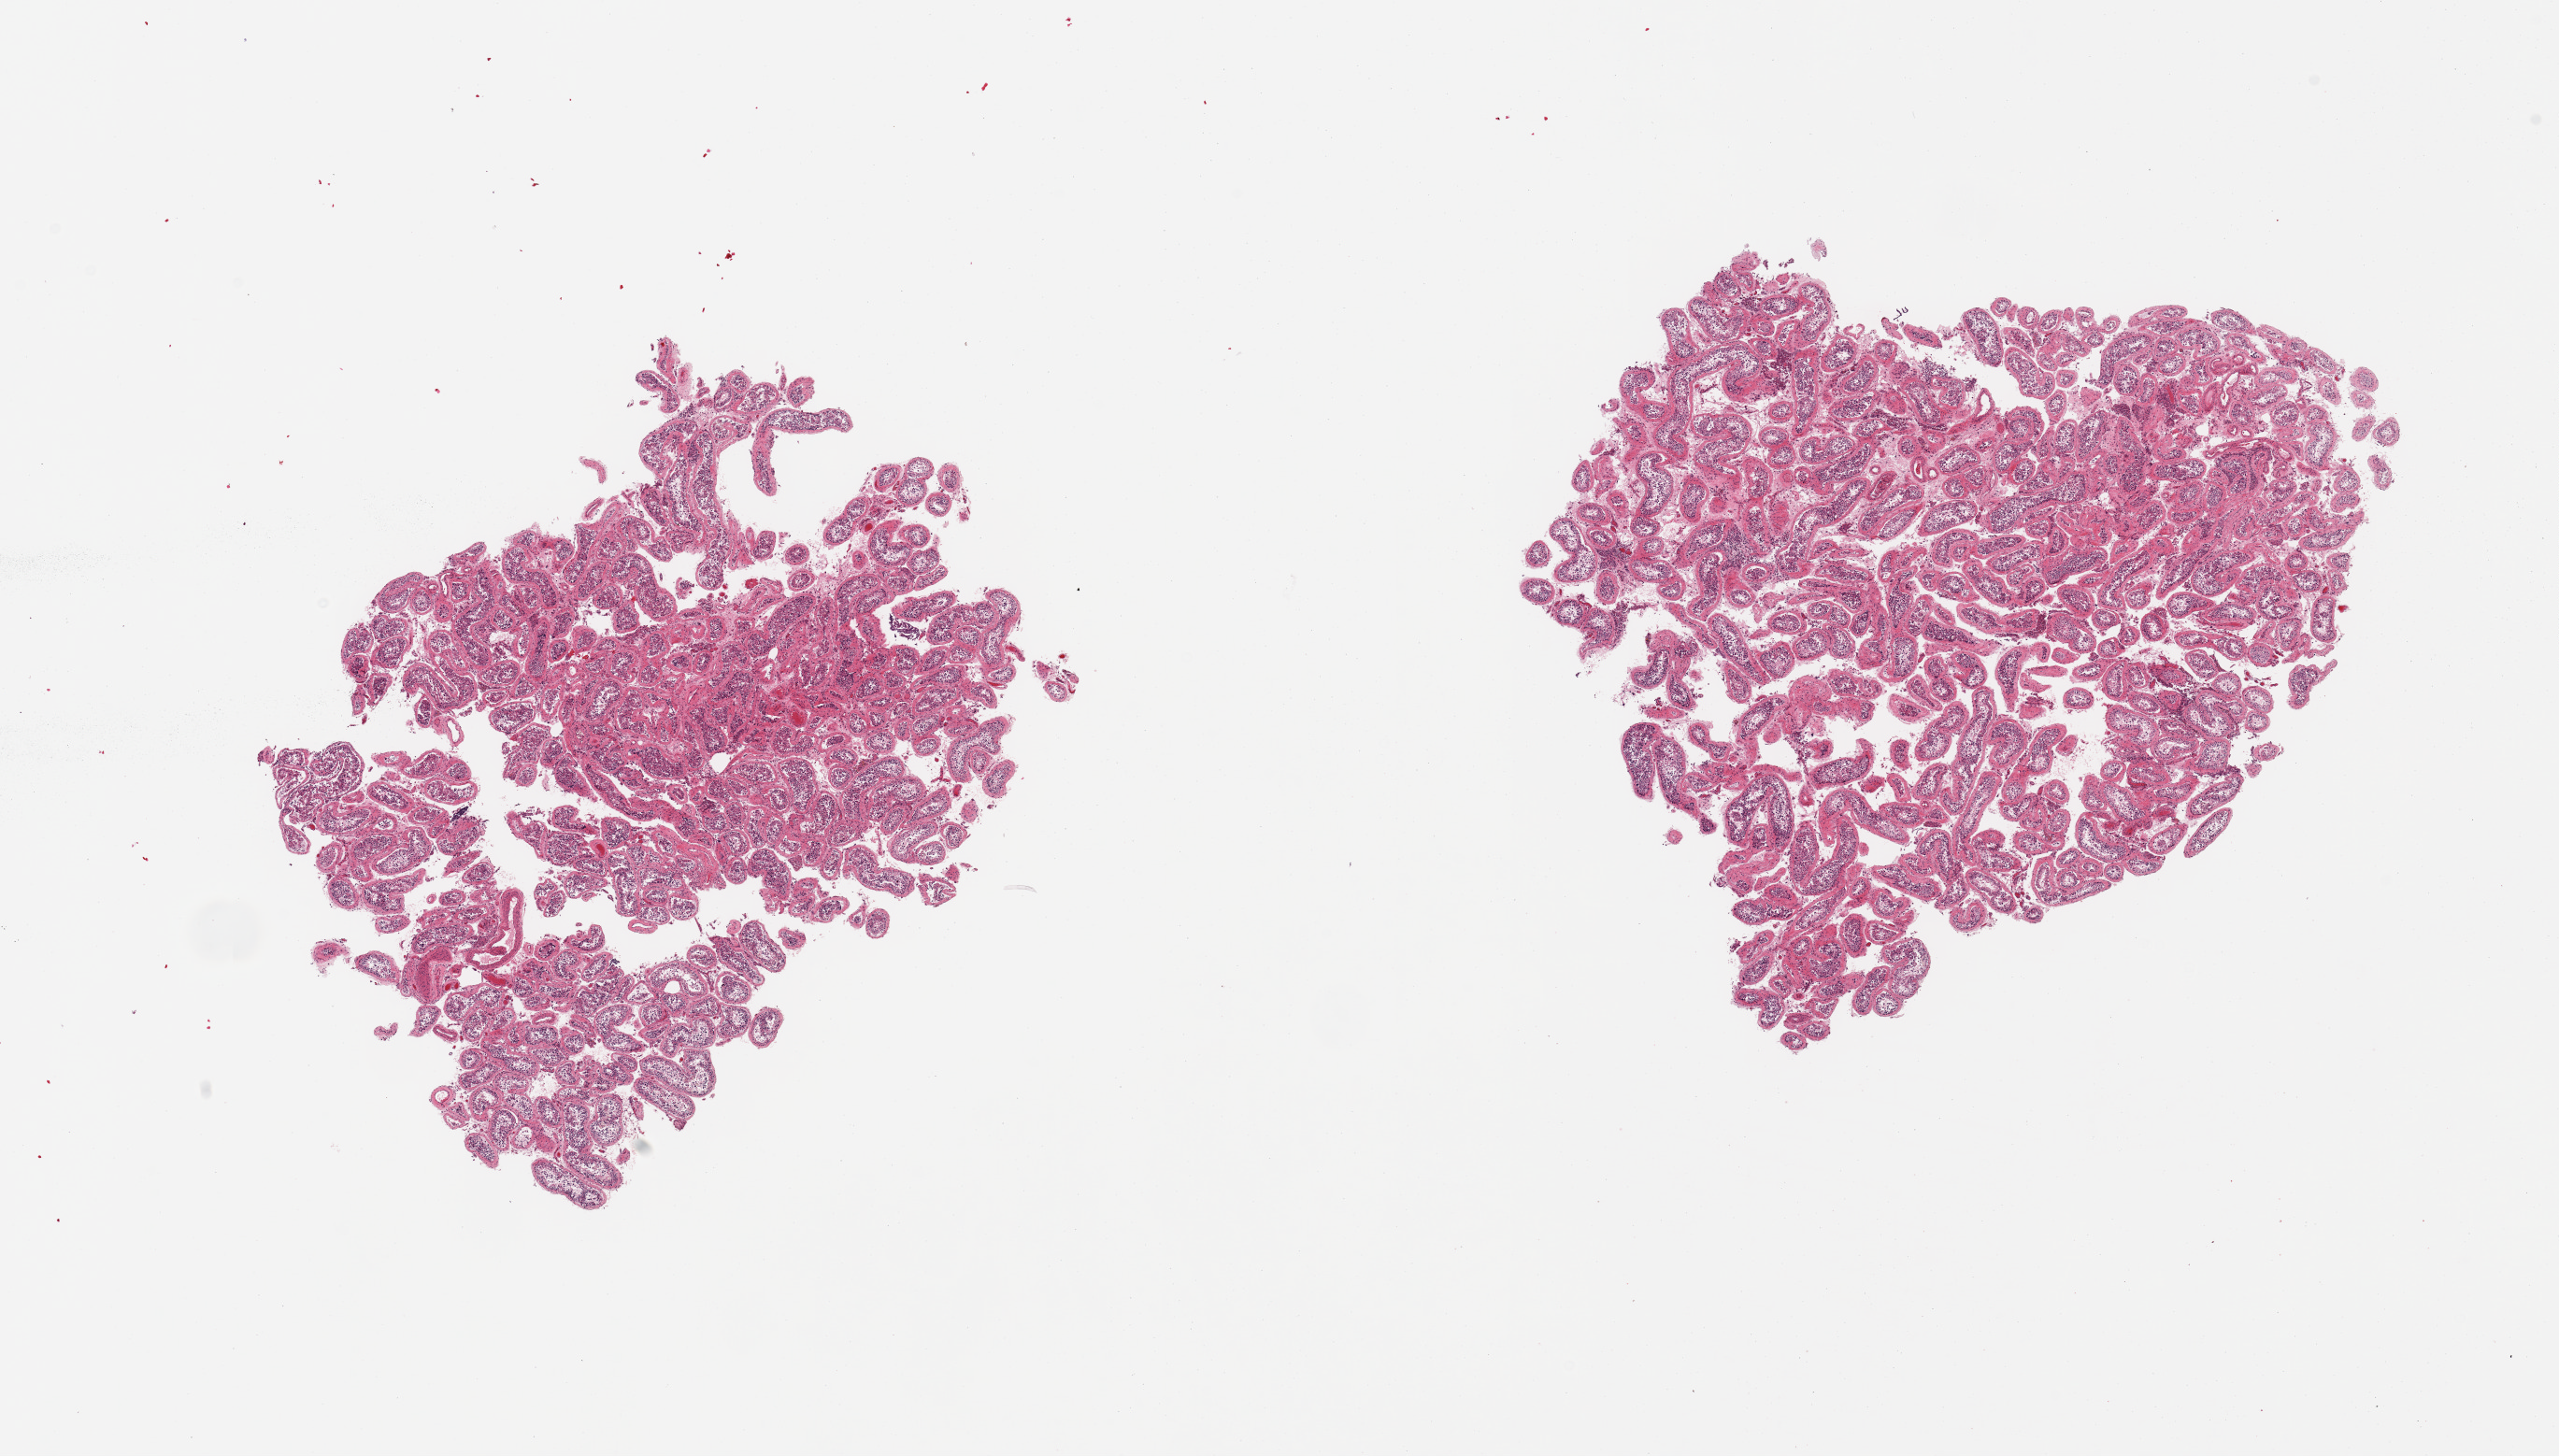
Whole-slide image, hematoxylin and eosin (H&E) stain — whole scanned area (about 21.7 x 12.3 mm) shown as a low-resolution overview. PAXgene-fixed paraffin-embedded (PFPE) section. Sampled site (target tissue): testis. Tissue donor sample. Male donor.
Review note (as recorded): 2 pieces, reduced spermatogenesis.